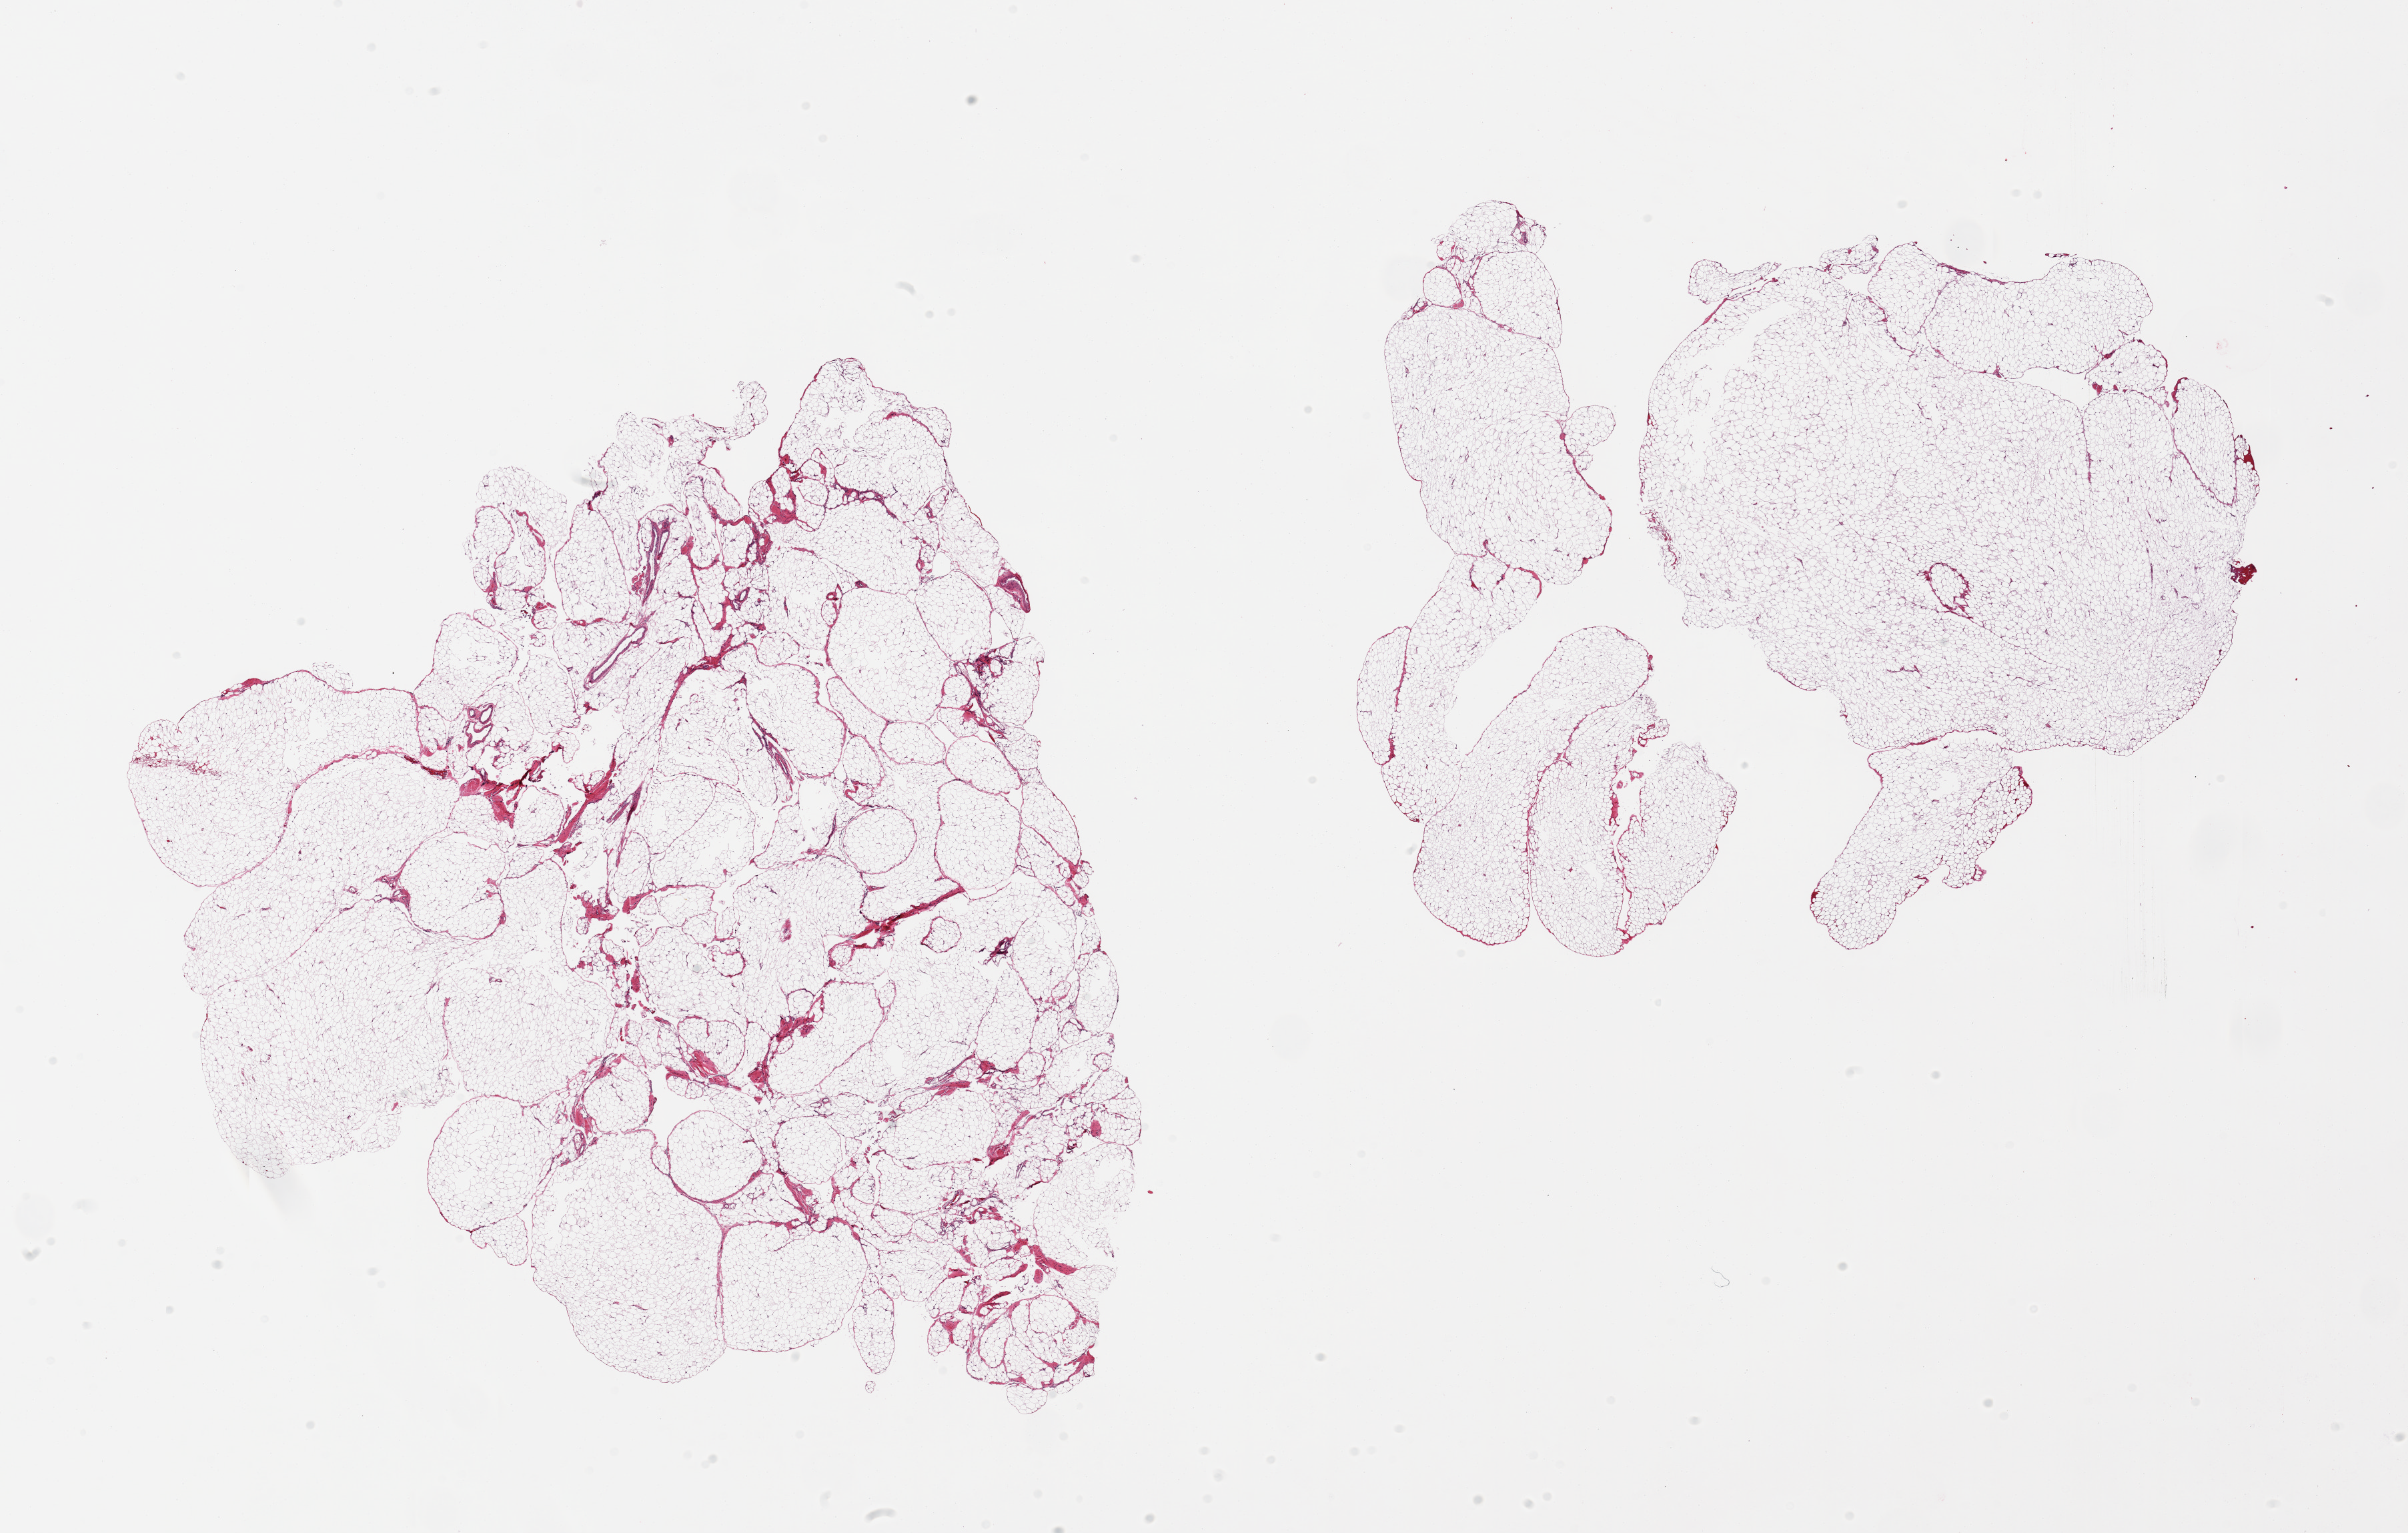
Whole-slide image, hematoxylin and eosin (H&E) stain, brightfield — a low-resolution overview of the entire scanned area, about 28.5 x 18.2 mm; PAXgene-fixed, paraffin-embedded tissue; section of omentum (target tissue); tissue donor sample. Male donor.
* reviewer comment on this tissue sample: 2 pieces